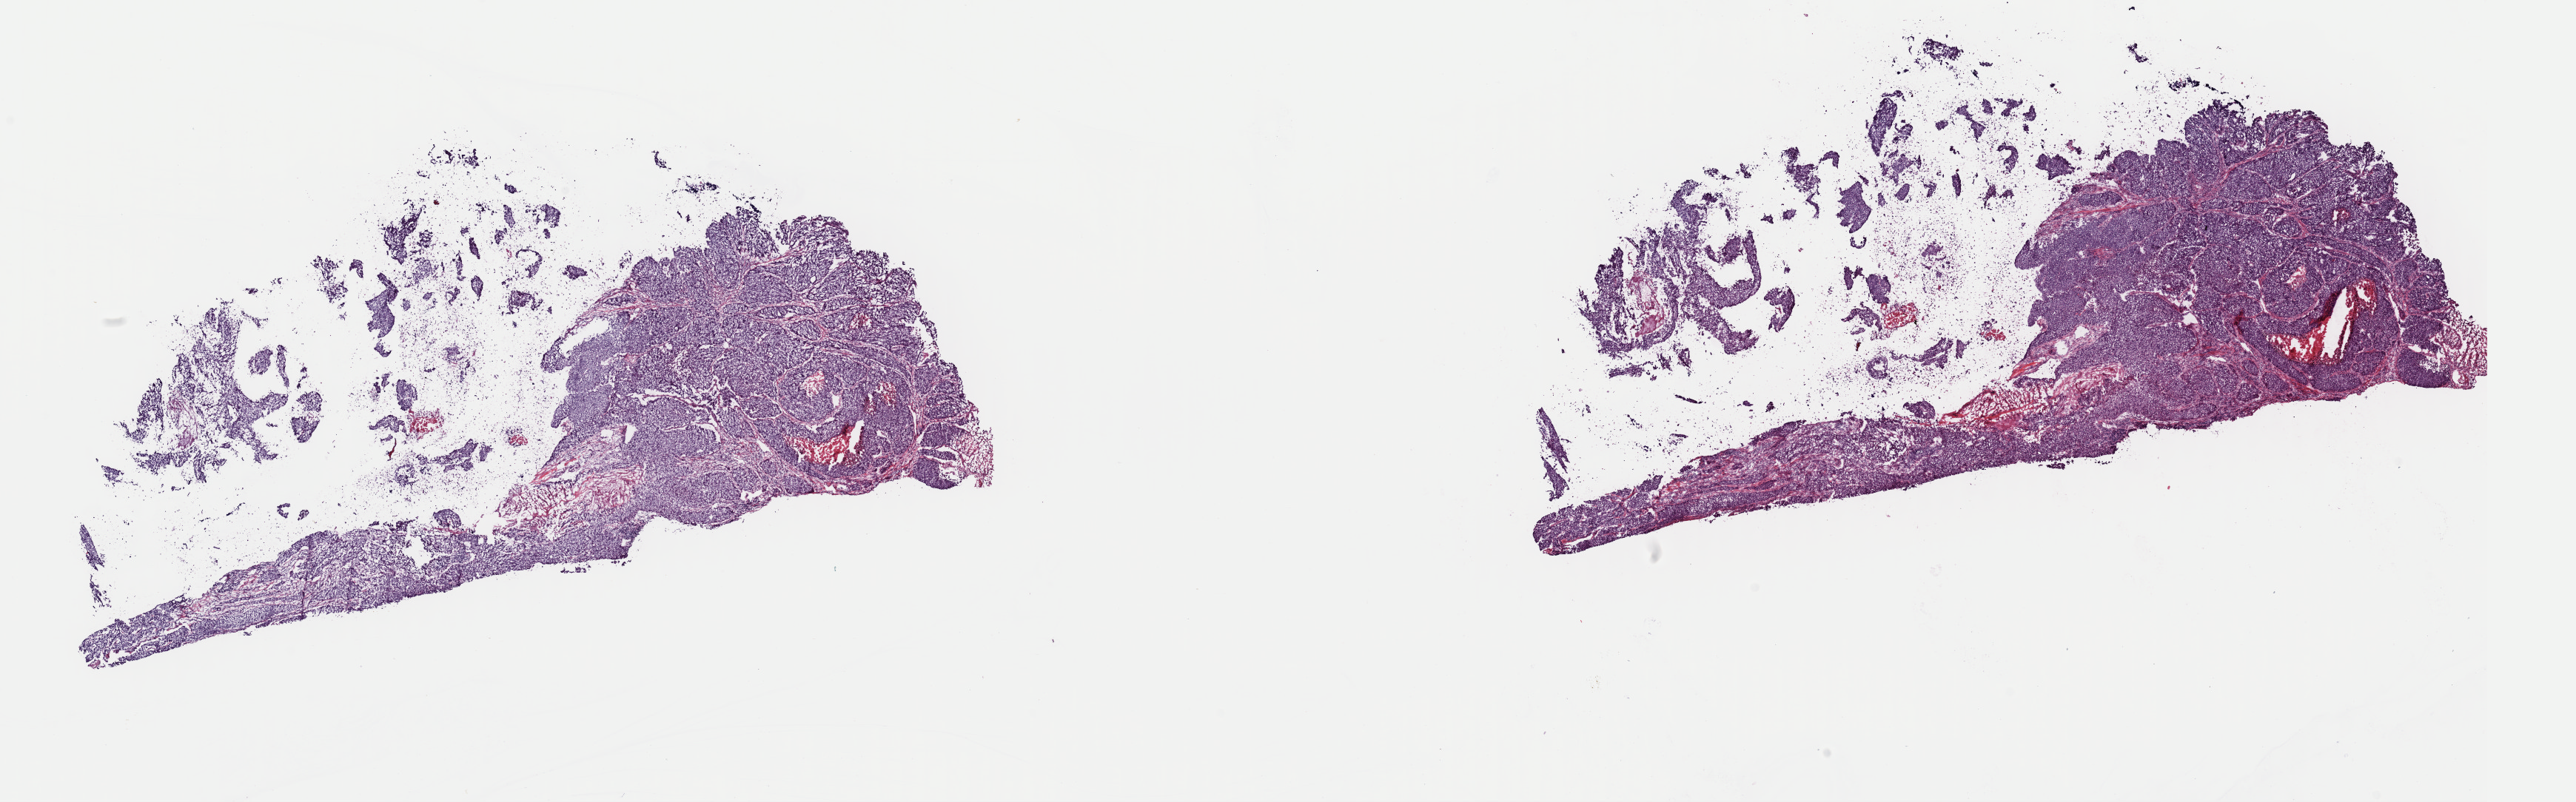
H&E whole-slide image — low-resolution overview of the scanned area, about 27.5 x 8.6 mm; frozen section; sample: primary tumour, bladder. Patient: male, age at initial diagnosis 54 years. Histologic grade: high grade. Composition of this section per pathologist review: tumour cells 70%, tumour nuclei 85%, normal cells 0%, stromal cells 23%, necrosis 7%. Infiltration values recorded for this section: lymphocyte infiltration 10%, monocyte infiltration 0%, neutrophil infiltration 1%.
Lymph nodes positive (case pathology): 2 of 38 examined. Pathologic diagnosis: Transitional cell carcinoma (trigone of bladder). AJCC pathologic stage: IV.